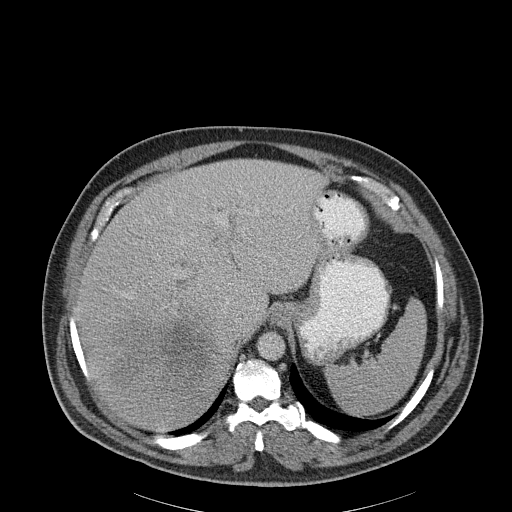
Contrast-enhanced abdominal CT, one axial slice. Slice 150 of 186 in the series (ordered by position). Reconstruction kernel B30f. 120 kVp. Soft-tissue window (W 400 / L 40 HU). 3 mm slice thickness. 512 × 512 image matrix. Patient: male, 56 years. Case-level facts recorded for this patient, not image findings: diagnosis: adrenocortical carcinoma; tumour side: right adrenal; tumour size at pathology: 18 cm; Ki-67 index: 2 %; stage (as recorded): 3.
Outlined on this slice (semi-automatic segmentation, software-assisted and operator-edited):
- mass: bounding box [x1, y1, x2, y2] px = [110, 320, 207, 383]